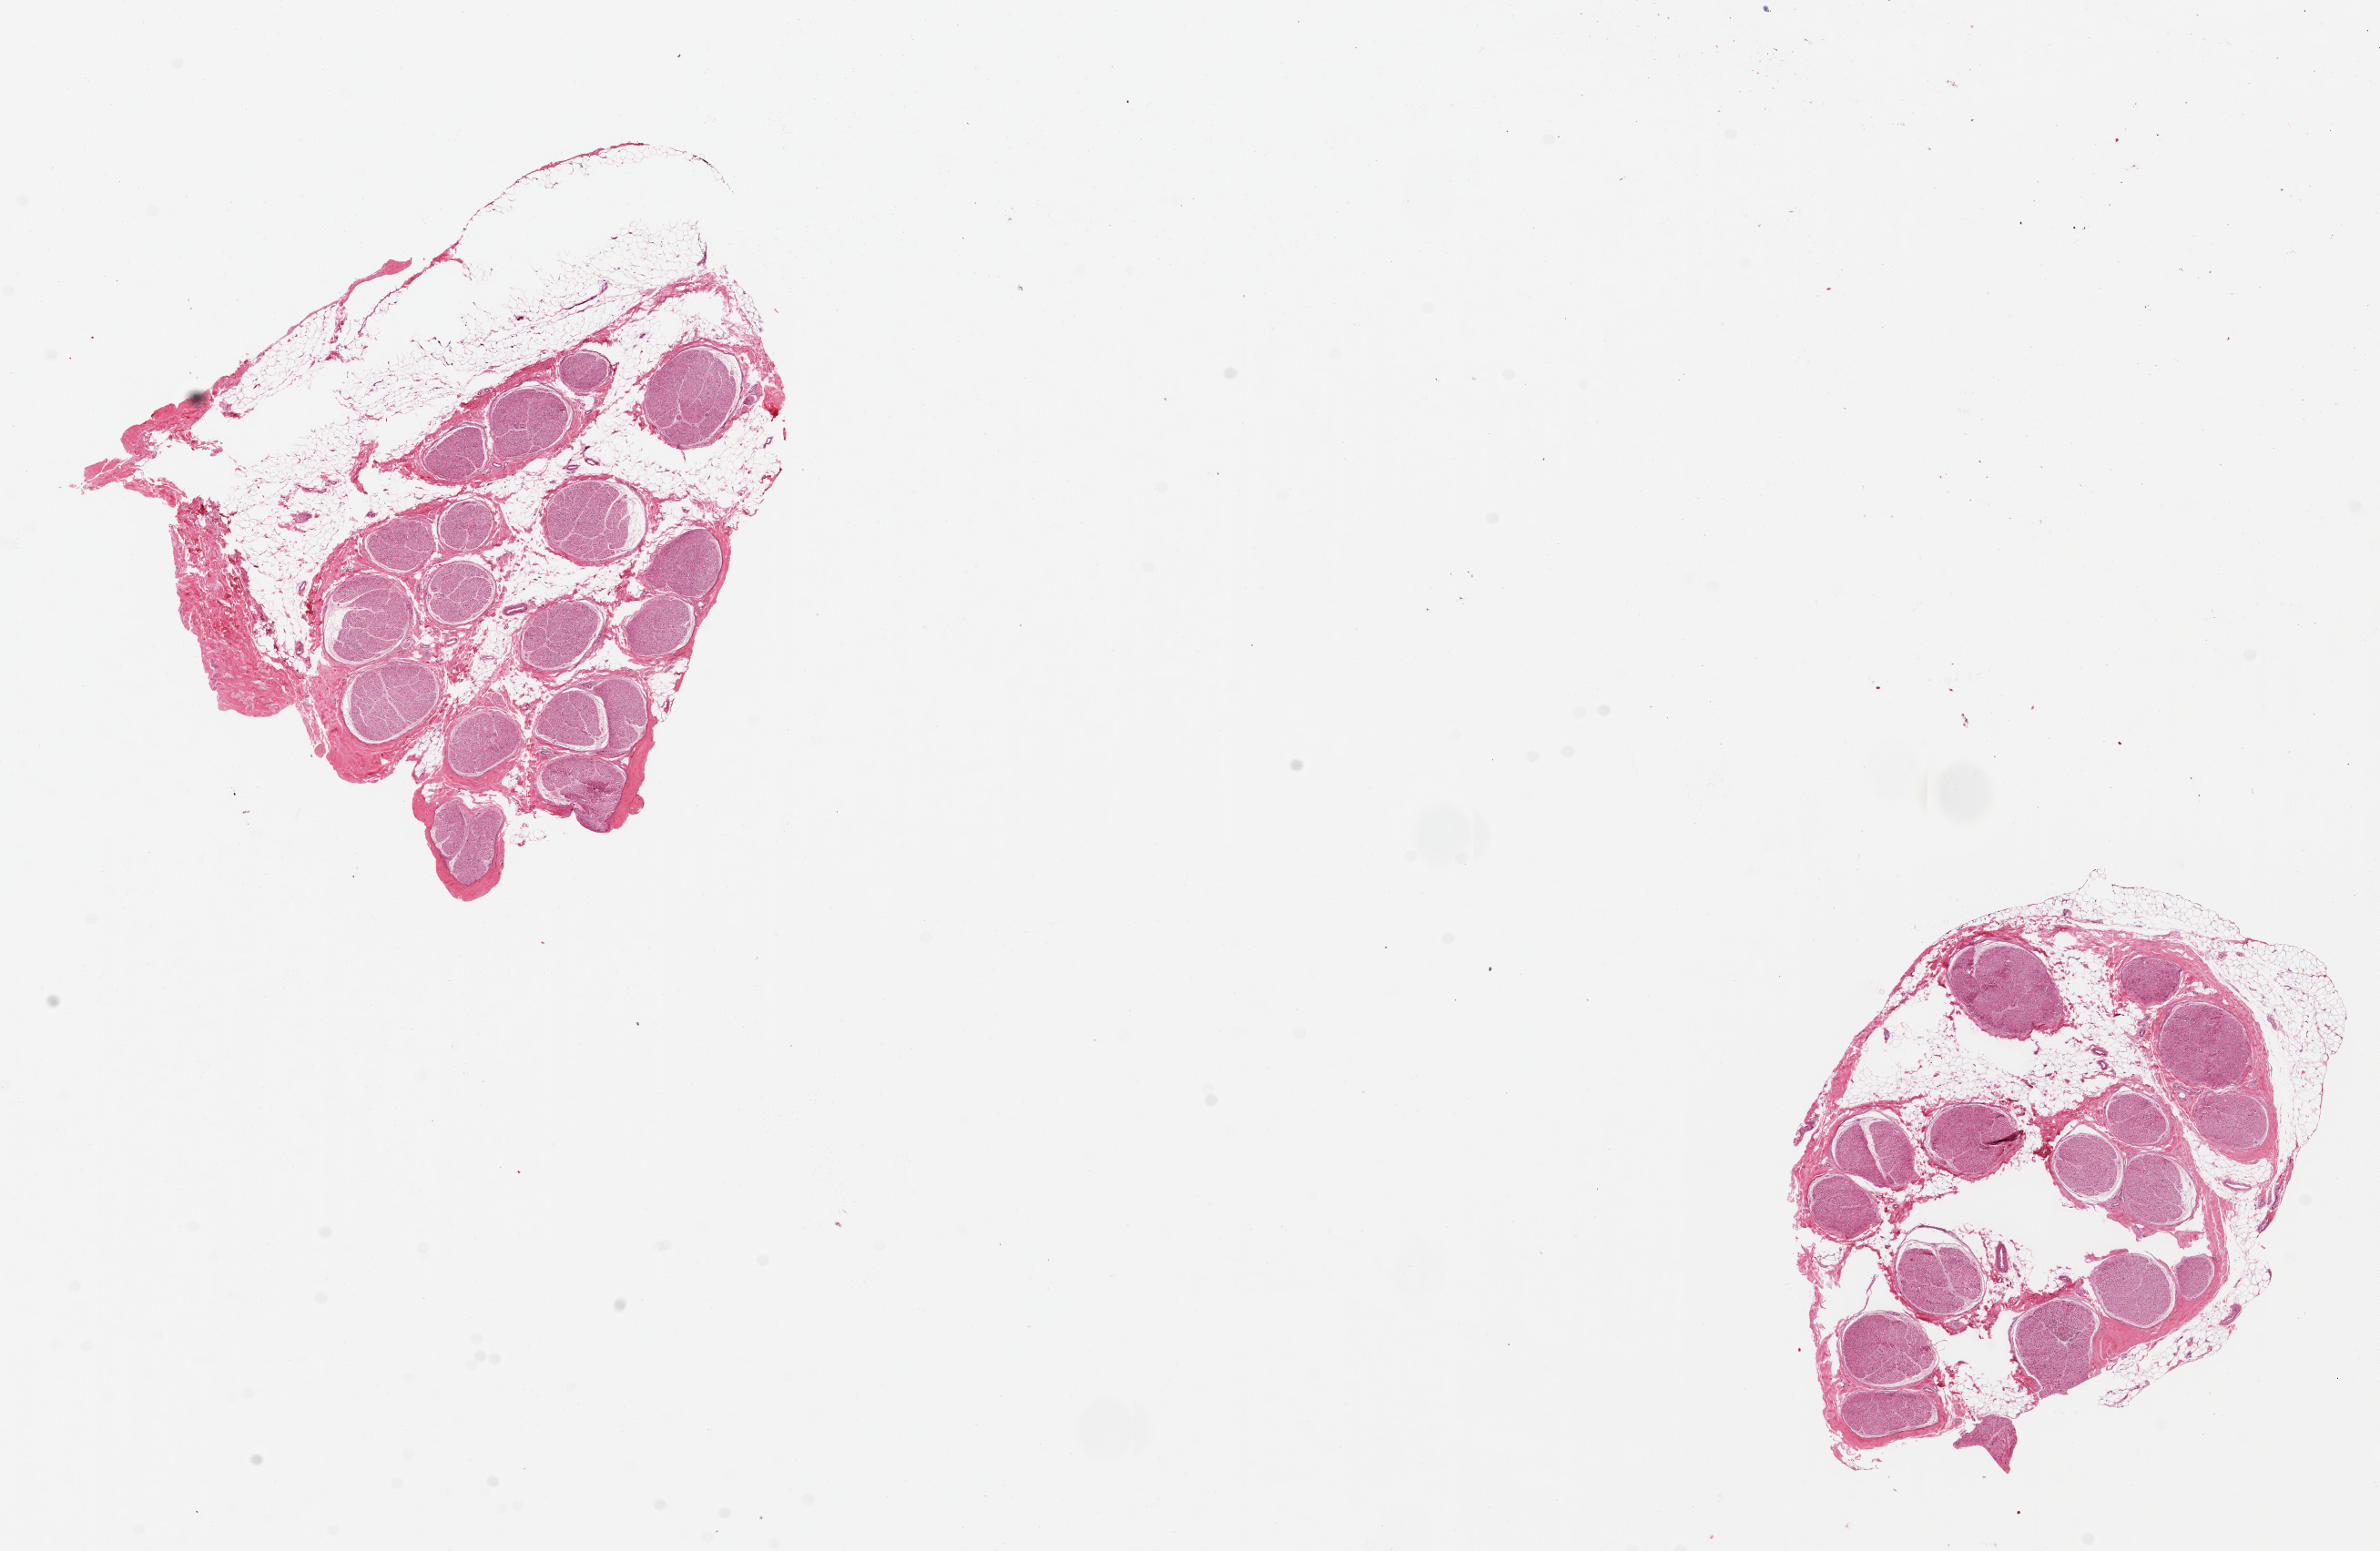
Whole-slide image, haematoxylin and eosin stain — shown as a low-resolution overview of the whole scanned area (about 20.7 x 13.5 mm, acquisition: 20x scan). PAXgene-fixed paraffin-embedded (PFPE) section. Sampled site (target tissue): tibial nerve. Donor tissue sample. Donor: male.
Reviewer comment on this tissue sample: 2 pieces, 6x5.5mm & 6x3.5mm; ~40% internal and external adipose tissue among nerve bundles.